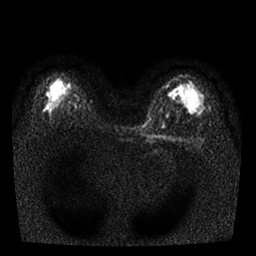
Breast MRI, one axial slice. Slice 17 of 25 in the series (ordered by position). Diffusion-weighted series; image 2 of 4 stored at this slice position (different b-values; order by instance number). 1.5 T. 4 mm slice thickness. 256 × 256 image matrix. Female patient.
Annotated regions visible in this slice (manually delineated by an expert):
- tumour on diffusion-weighted imaging: bounding box <47,94,49,96> (left, top, right, bottom; pixels)